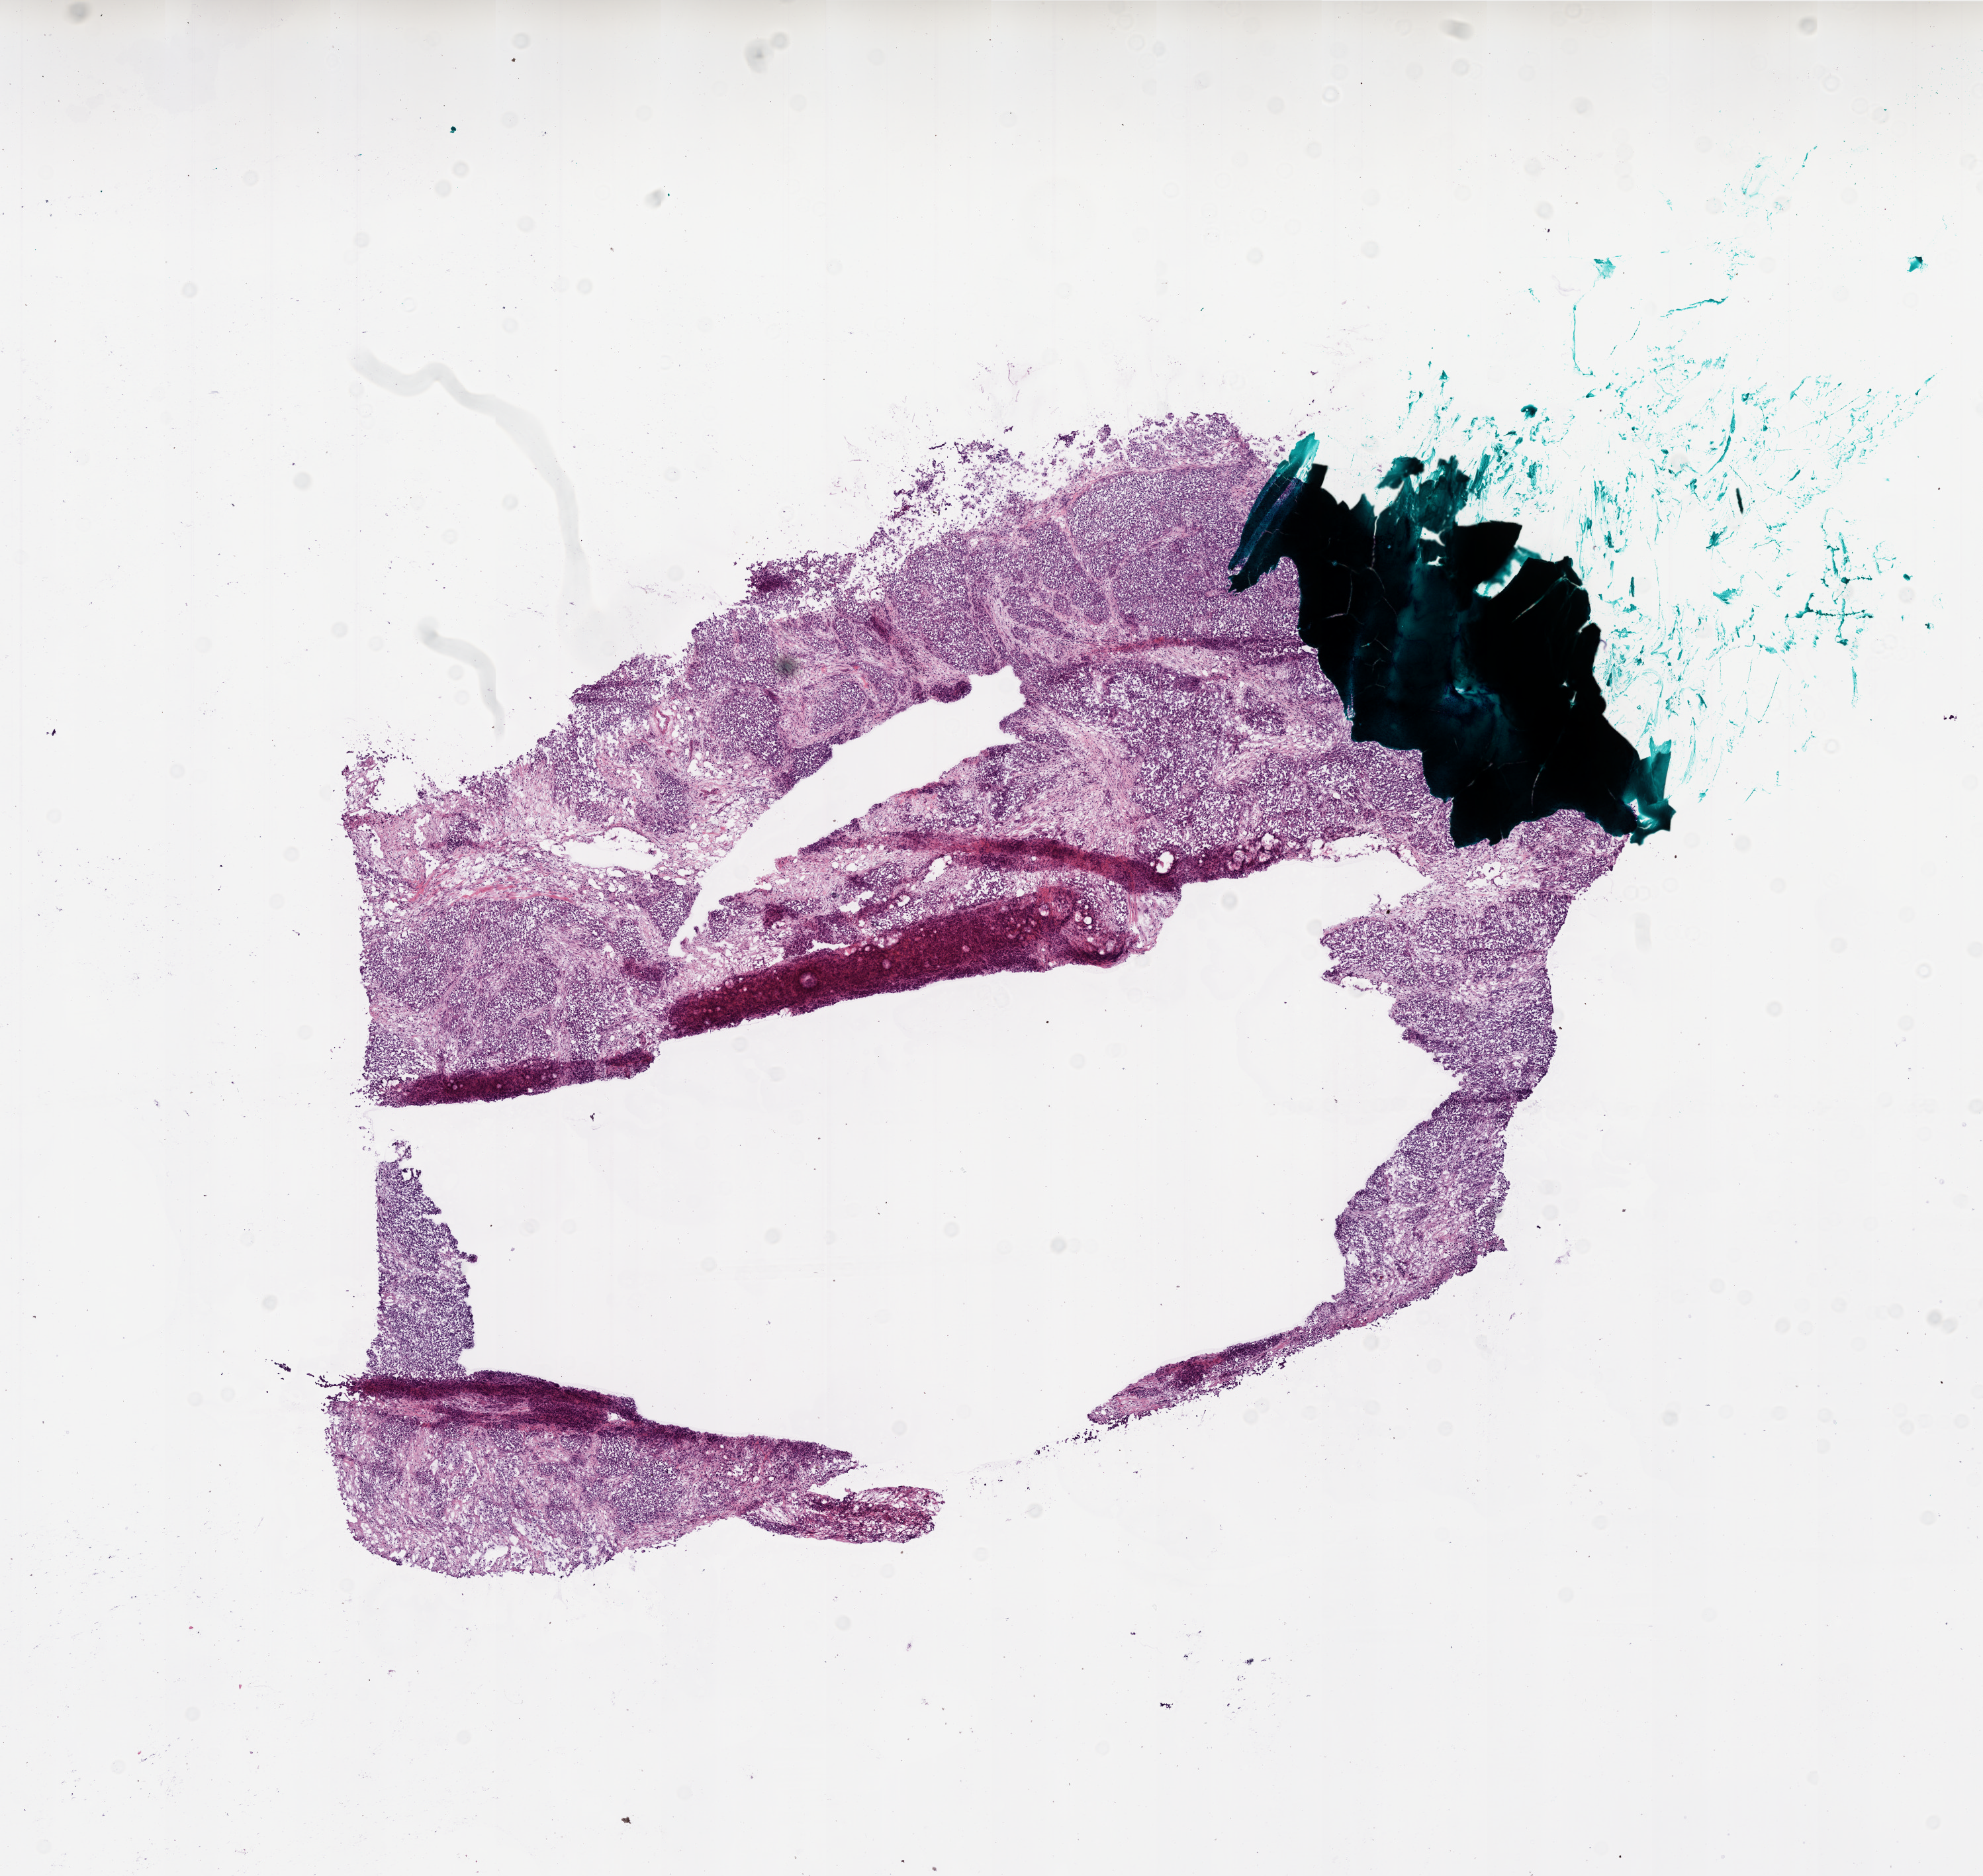
Whole-slide histology image, H&E — whole scanned area (about 12.0 x 11.3 mm) shown as a low-resolution overview, frozen section, sample: primary tumour, ovary. Female patient; age at initial diagnosis 70 years. Histologic grade: G3 (poorly differentiated). Pathologist review of this section (percent, as recorded): tumour cells 78%, tumour nuclei 80%, normal cells 19%, stromal cells 1%, necrosis 2%. Inflammatory infiltration, as recorded: lymphocyte infiltration 90%.
Laterality: left. Histologic diagnosis: Serous cystadenocarcinoma, NOS. FIGO stage: IIIC.